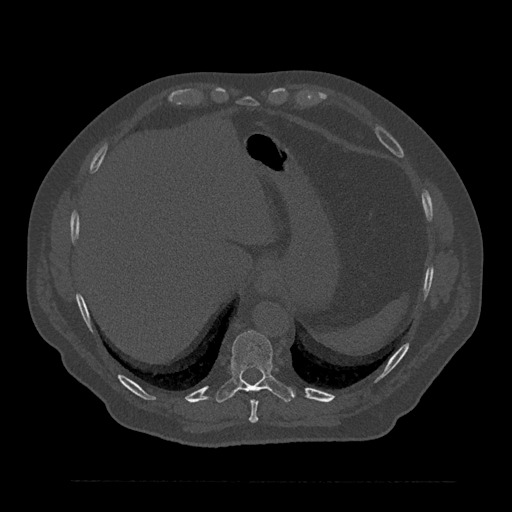
CT including the spine, one axial slice. Position 362 of 797 along the scan axis. Reconstruction kernel Br40s/3. Bone window (W 1800 / L 400 HU). 0.5 mm slice thickness. 512 × 512 image matrix, field of view 430 × 430 mm. Patient: male, 61 years. Case-level facts recorded for this patient, not image findings: primary cancer: prostate.
Annotated regions visible in this slice (semi-automatically segmented with operator editing):
- T10 vertebra: bounding box [x1, y1, x2, y2] px = [216, 331, 295, 403]
- T9 vertebra: [249, 399, 258, 423]